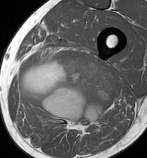
MRI of an extremity soft-tissue mass, one axial slice. Slice 59 of 86 in the series (ordered by position). MR volume resampled by the dataset authors to the PET/CT grid (not the native acquisition matrix). 3.27 mm slice thickness. 147 × 158 image matrix, field of view 144 × 154 mm. Male patient. From the clinical record (not read from this slice): histological type: undifferentiated pleomorphic liposarcoma; grade: high; site of the primary tumour: left thigh.
Annotated regions visible in this slice (expert contour drawn on MRI and transferred to this co-registered scan by the dataset authors):
- gross tumour volume including surrounding oedema: box from (x=19, y=51) to (x=116, y=130) px
- gross tumour volume (mass): (x=19, y=51)–(x=116, y=125)